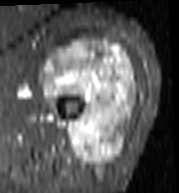
MRI of an extremity soft-tissue mass, one axial slice. STIR. MR volume resampled by the dataset authors to the PET/CT grid (not the native acquisition matrix). 3.27 mm slice thickness. 179 × 193 image matrix, field of view 175 × 188 mm. Female patient. Case-level facts recorded for this patient, not image findings: histological type: undifferentiated – high grade; grade: high; site of the primary tumour: left thigh.
Annotated regions visible in this slice (expert contour drawn on MRI and transferred to this co-registered scan by the dataset authors):
- gross tumour volume including surrounding oedema: box from (x=41, y=37) to (x=138, y=170) px
- gross tumour volume (mass): (x=41, y=37)–(x=138, y=170)